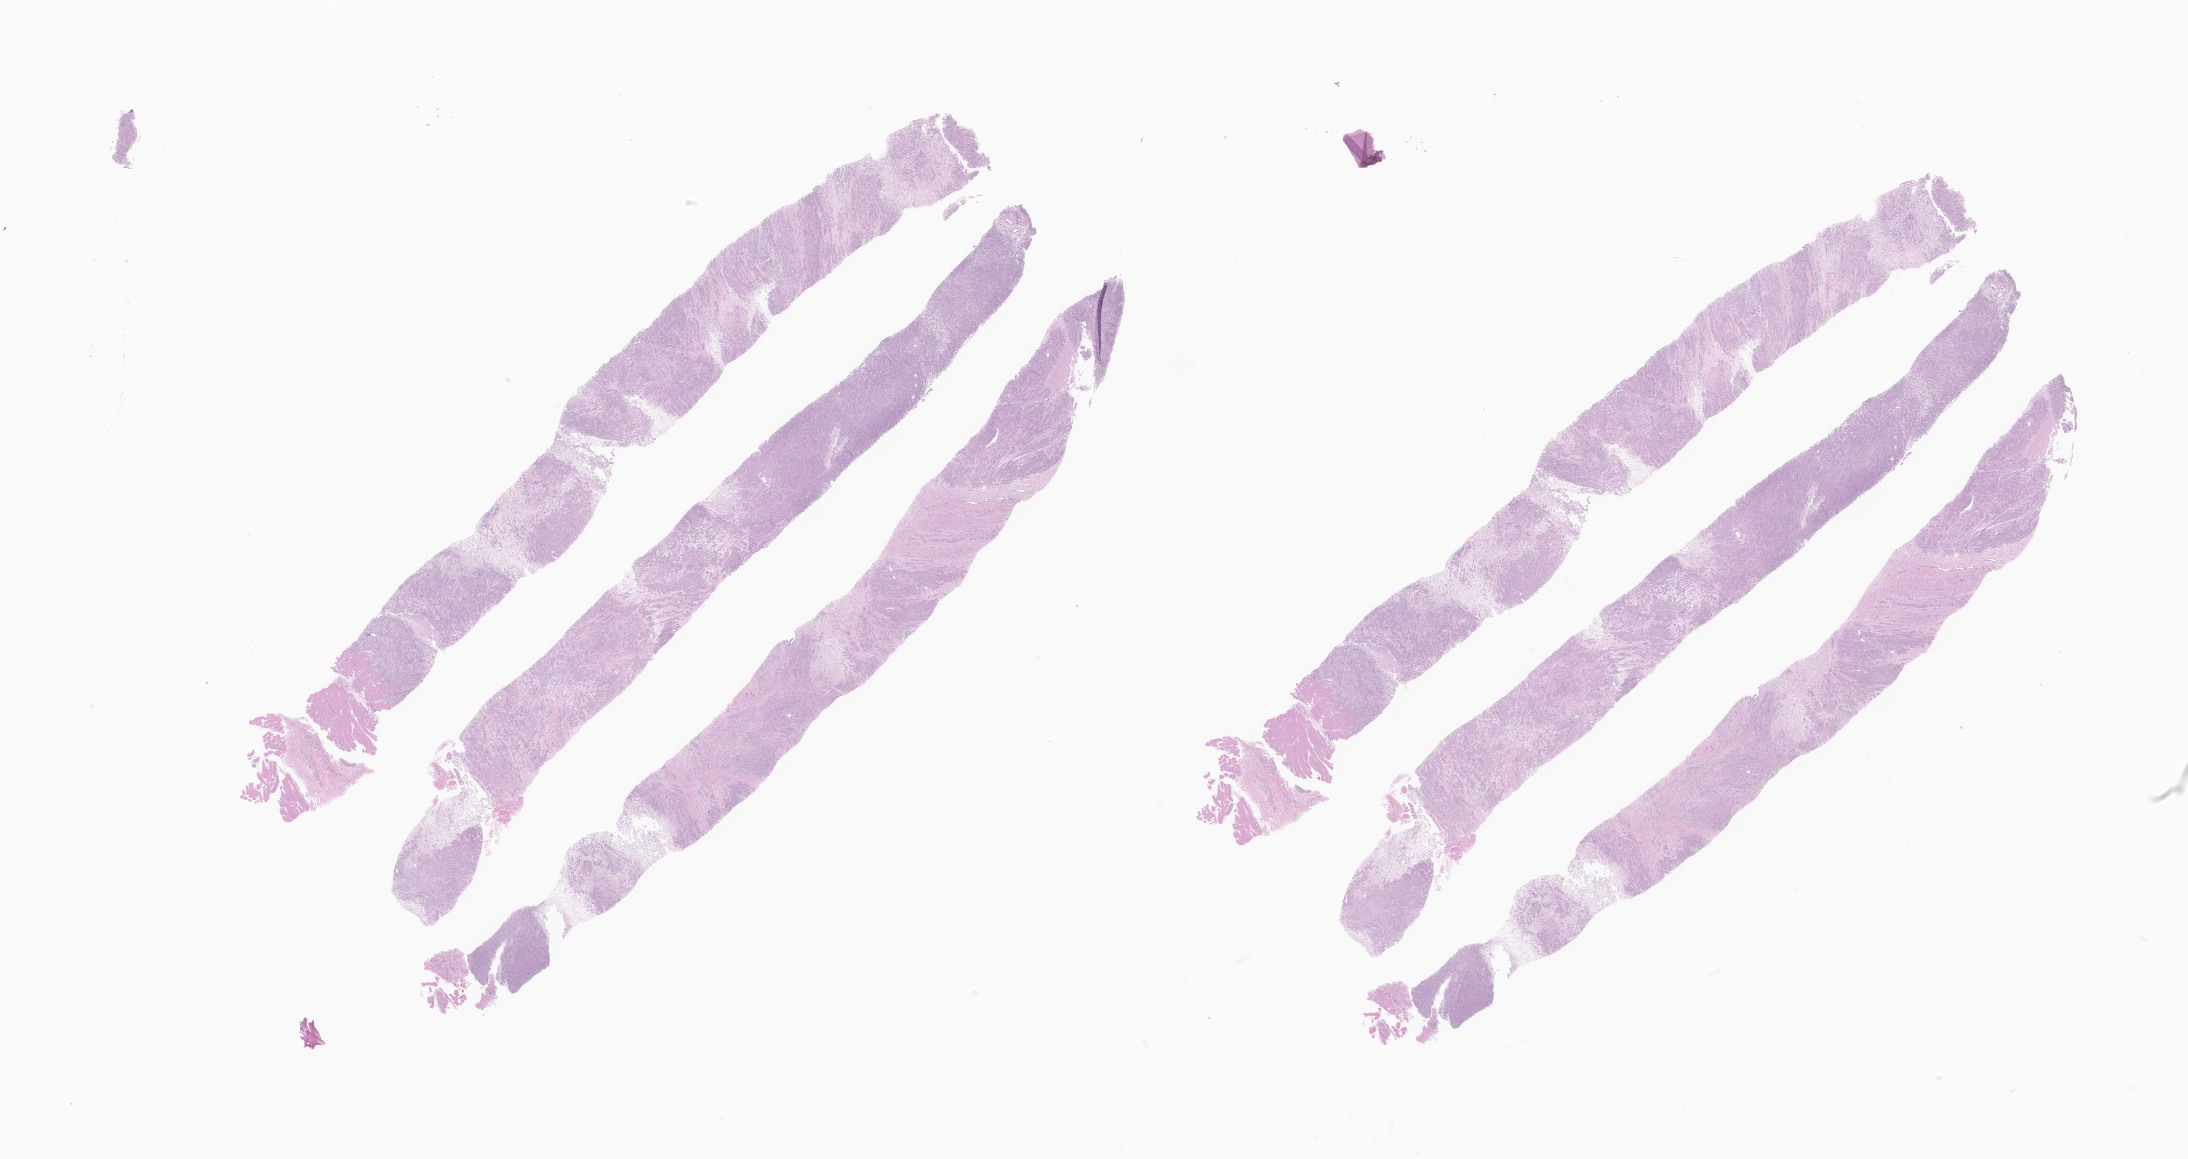
Digitized hematoxylin and eosin (H&E)-stained section of tumor tissue from the soft tissue of lower extremity — shown as a low-resolution overview of the whole scanned area (about 36.9 x 19.5 mm), FFPE section. Patient female; age 249 months (20 years 9 months).
- diagnosis: Epithelioid sarcoma, NOS